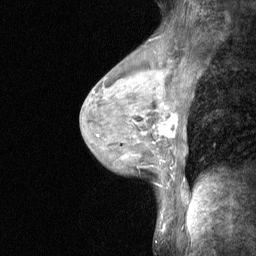
Breast MRI (dynamic contrast-enhanced), one sagittal slice. Slice 37 of 64 in the series (ordered by position). Dynamic contrast-enhanced study with each time point stored as its own series, time point 2 of 3 at this slice position (early post-contrast, ordered by acquisition time). 1.5 T. TE 4.8 ms, TR 27 ms. 2 mm slice thickness. 256 × 256 image matrix, field of view 200 × 200 mm. Patient: female, 44 years. From the clinical record (not read from this slice): setting: breast cancer imaged before/during neoadjuvant chemotherapy; receptor status: HR-positive, HER2-negative.
Annotated regions visible in this slice (semi-automatically segmented with operator editing):
- analysis volume of interest (the breast-tissue region the enhancement analysis was run in; not a lesion): box from (x=140, y=109) to (x=180, y=148) px
- tumour enhancement mask (voxels above the 90 % enhancement threshold inside the analysis volume of interest): (x=160, y=115)–(x=177, y=137)